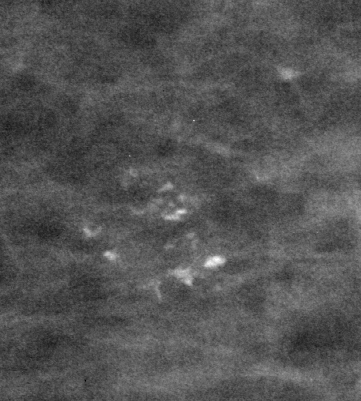
Crop from a digitized film mammogram around one marked abnormality, left breast, CC view.
- Finding: calcifications, morphology pleomorphic, distribution clustered; BI-RADS assessment category 4; pathology result (as recorded, not read from the image): benign.